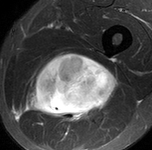
MRI of an extremity soft-tissue mass, one axial slice; position 72 of 90 along the scan axis; STIR; MR volume resampled by the dataset authors to the PET/CT grid (not the native acquisition matrix); 3.27 mm slice thickness; 152 × 150 image matrix. Male patient. From the clinical record (not read from this slice): histological type: undifferentiated pleomorphic liposarcoma; grade: high; site of the primary tumour: left thigh.
Structures marked on this image (expert contour drawn on MRI and transferred to this co-registered scan by the dataset authors):
- gross tumour volume including surrounding oedema: box from (x=23, y=53) to (x=119, y=124) px
- gross tumour volume (mass): (x=34, y=53)–(x=119, y=115)